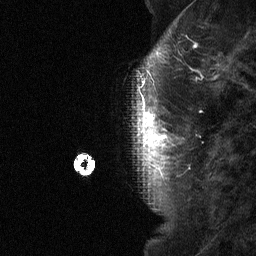
Breast MRI (dynamic contrast-enhanced), one sagittal slice. Position 15 of 64 along the scan axis. Dynamic contrast-enhanced study with each time point stored as its own series, time point 2 of 3 at this slice position (early post-contrast, ordered by acquisition time). 1.5 T. TE 4.8 ms, TR 27 ms. 256 × 256 image matrix, field of view 180 × 180 mm. Female patient, age 42 years. From the clinical record (not read from this slice): setting: breast cancer imaged before/during neoadjuvant chemotherapy; receptor status: triple-negative.
Structures marked on this image (semi-automatically segmented with operator editing):
- analysis volume of interest (the breast-tissue region the enhancement analysis was run in; not a lesion): bounding box [x1, y1, x2, y2] px = [130, 85, 183, 160]
- tumour enhancement mask (voxels above the 90 % enhancement threshold inside the analysis volume of interest): [141, 112, 166, 143]